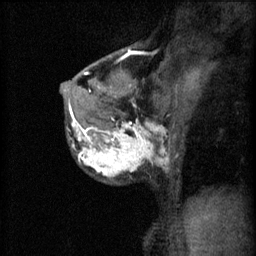
Breast MRI (dynamic contrast-enhanced), one sagittal slice. 3 images stored at this slice position (order not interpretable as contrast timing). 1.5 T. TE 4.2 ms, TR 11 ms. 2 mm slice thickness. 256 × 256 image matrix. Patient: female, 37 years.
Outlined on this slice (semi-automatic segmentation, software-assisted and operator-edited):
- analysis volume of interest (the breast-tissue region the enhancement analysis was run in; not a lesion): bounding box <68,118,175,185> (left, top, right, bottom; pixels)
- tumour enhancement mask (voxels above the 70 % enhancement threshold inside the analysis volume of interest): <72,122,168,177>